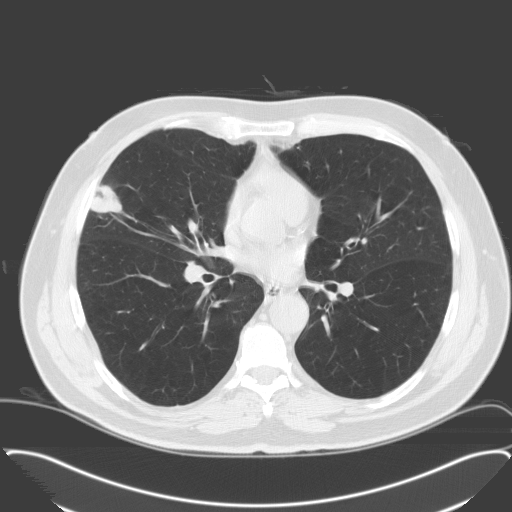
Low-dose screening chest CT, one axial slice; position 92 of 174 along the scan axis; 120 kVp; lung window (W 1500 / L -600 HU); 512 × 512 image matrix, field of view 400 × 400 mm.
Annotated regions visible in this slice (expert manual segmentation):
- lesion 1 (tumor, middle lobe of right lung): box from (x=91, y=185) to (x=122, y=213) px